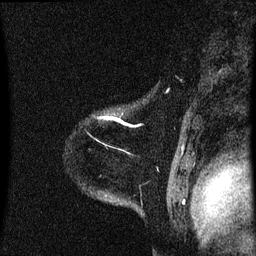
Breast MRI (dynamic contrast-enhanced), one sagittal slice; position 55 of 60 along the scan axis; dynamic contrast-enhanced series, image 2 of 3 at this slice position (ordered by acquisition); 1.5 T; TE 4.2 ms, TR 8.4 ms; 2 mm slice thickness; 256 × 256 image matrix, field of view 200 × 200 mm. Female patient, age 35 years. Case-level facts recorded for this patient, not image findings: setting: breast cancer imaged before/during neoadjuvant chemotherapy; receptor status: HER2-positive.
Structures marked on this image (semi-automatic segmentation, software-assisted and operator-edited):
- analysis volume of interest (the breast-tissue region the enhancement analysis was run in; not a lesion): bounding box <86,108,174,173> (left, top, right, bottom; pixels)
- tumour enhancement mask (voxels above the 70 % enhancement threshold inside the analysis volume of interest): <98,116,126,125>